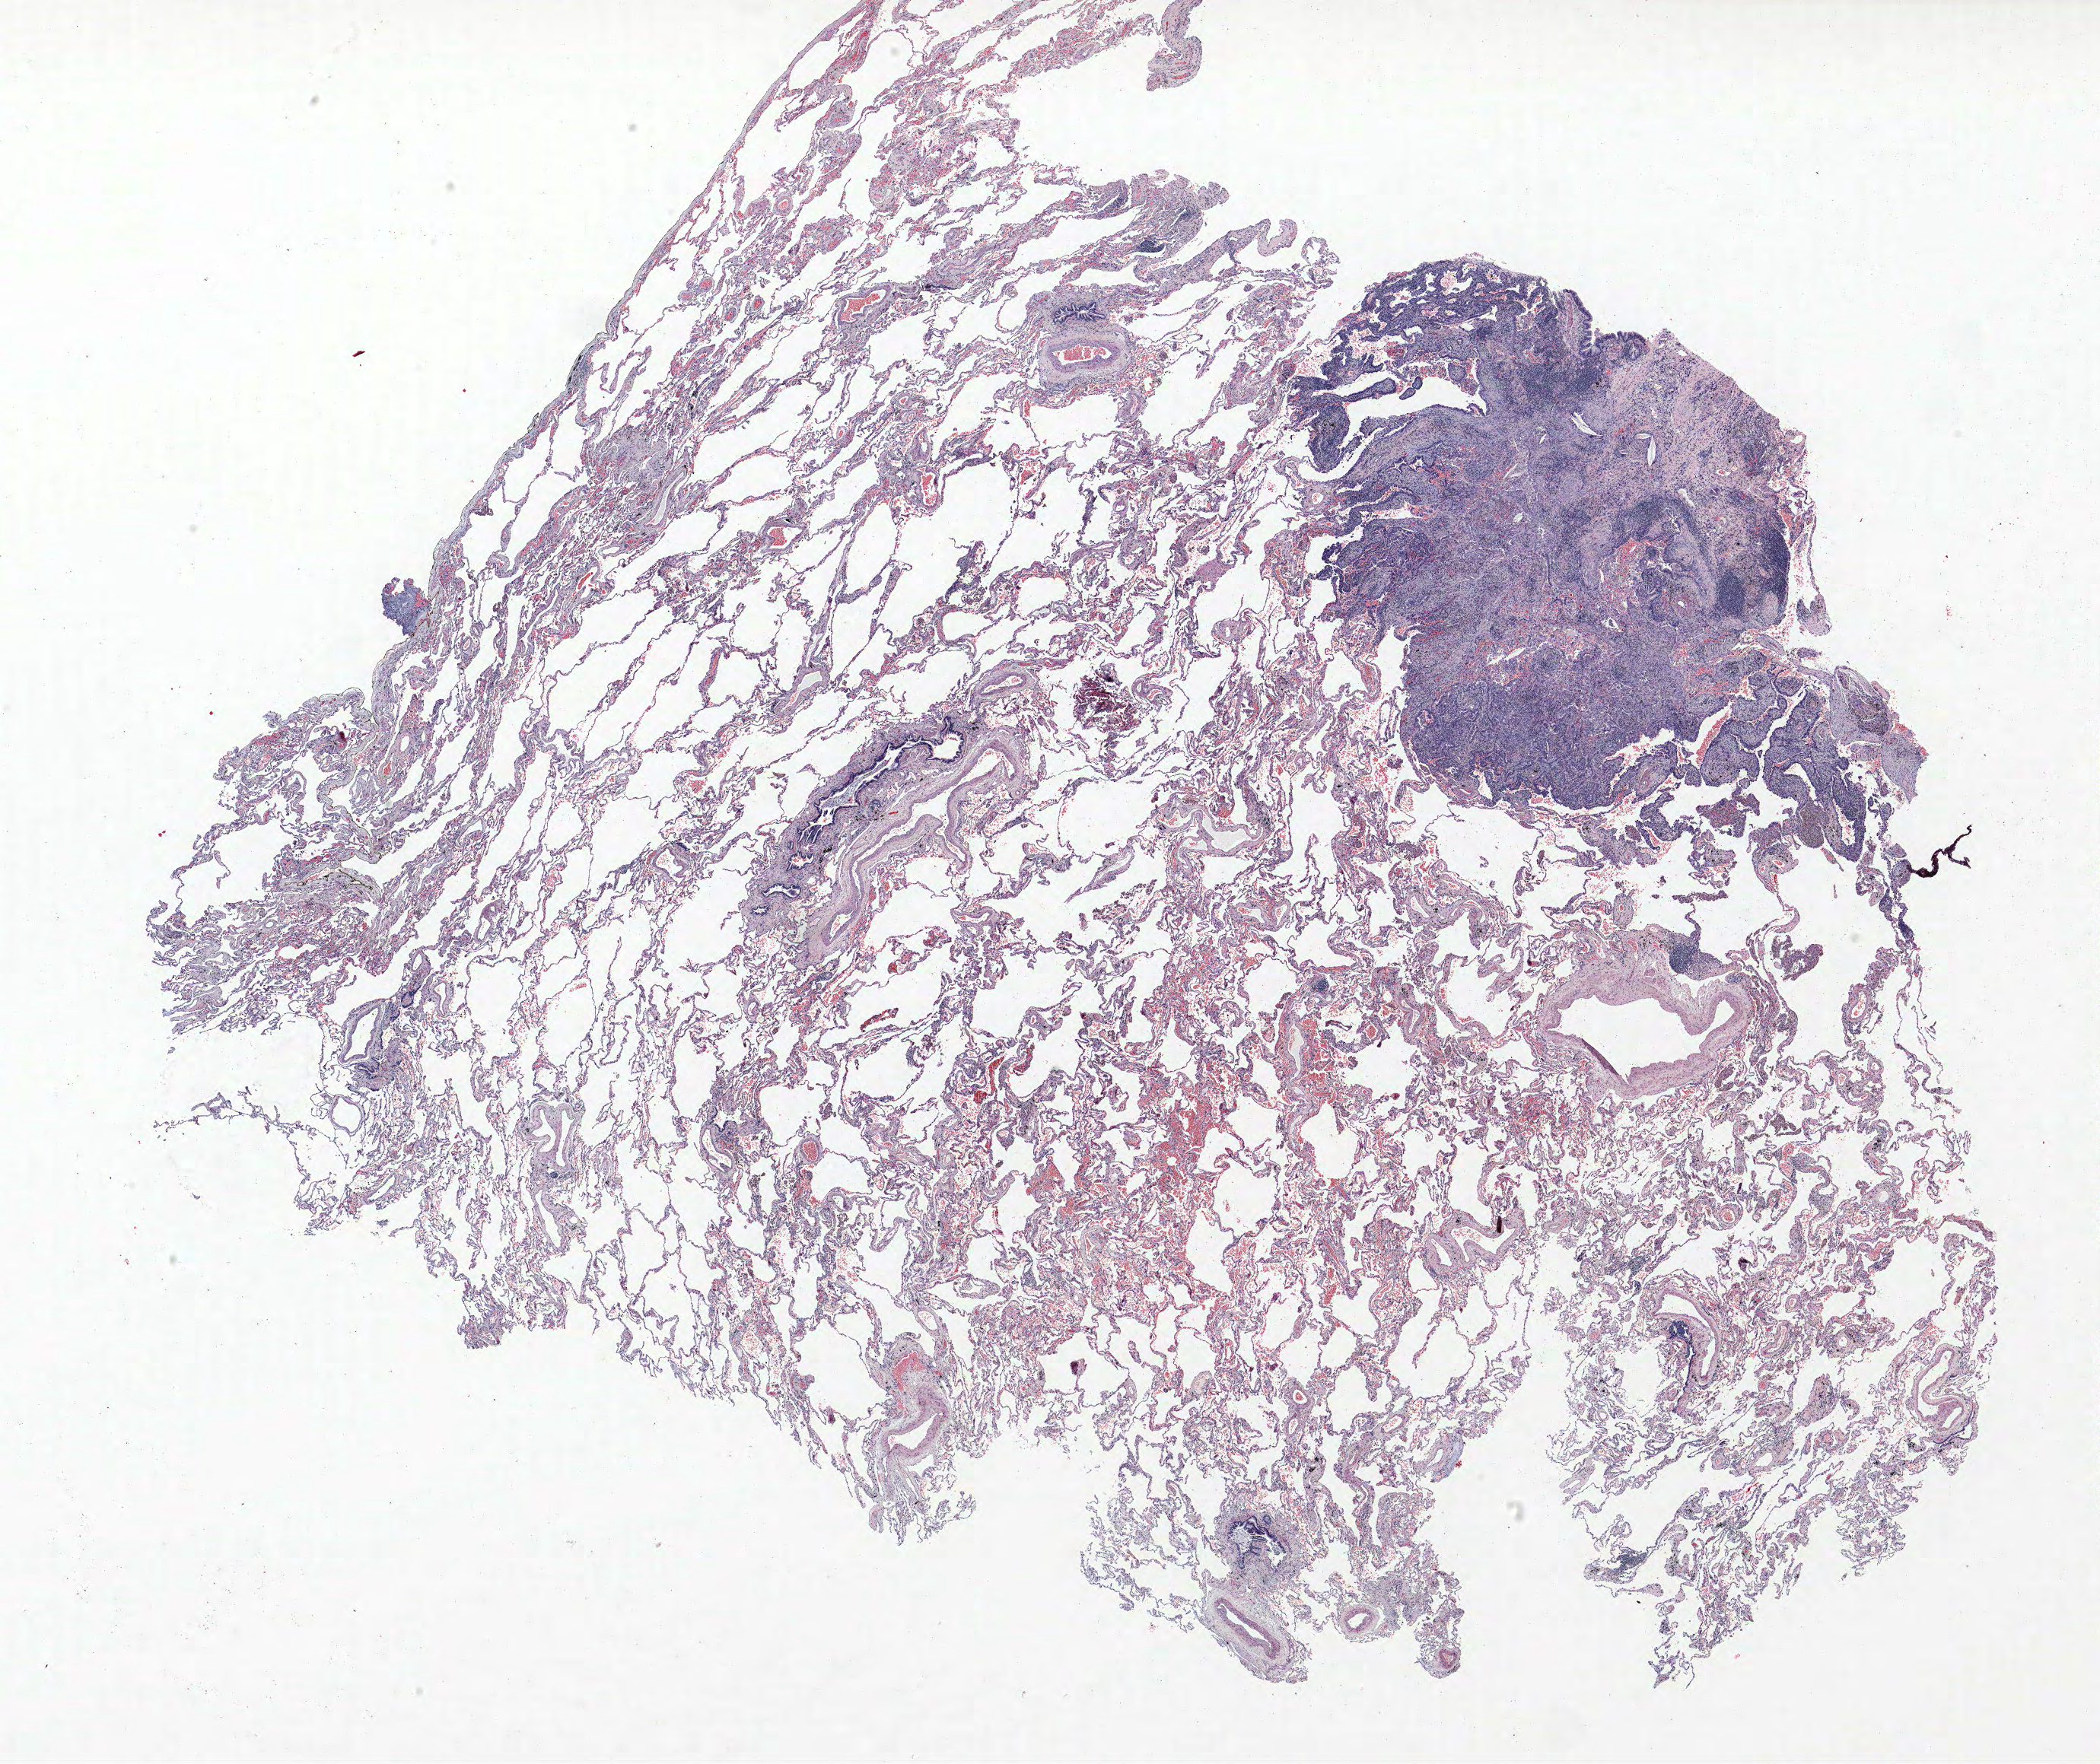
H&E-stained whole-slide image — whole scanned area (about 22.1 x 18.6 mm) shown as a low-resolution overview, formalin-fixed paraffin-embedded (FFPE) section, lung. Female patient, aged 60 at enrolment. Current smoker at enrolment. Grade: well differentiated (G1).
Stage (AJCC 6th edition): IA. Primary tumour location (clinical record): left lower lobe. Participant's lung-cancer diagnosis: Adenocarcinoma, NOS. Tumour size (pathology): 15 mm.